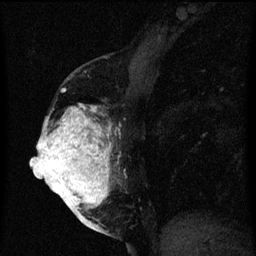
Breast MRI (dynamic contrast-enhanced), one sagittal slice. Position 26 of 60 along the scan axis. Dynamic contrast-enhanced series, image 2 of 3 at this slice position (ordered by acquisition). 1.5 T. TE 4.2 ms, TR 8 ms. 2 mm slice thickness. 256 × 256 image matrix, field of view 180 × 180 mm. Patient: female, 56 years.
Annotated regions visible in this slice (semi-automatic segmentation, software-assisted and operator-edited):
- analysis volume of interest (the breast-tissue region the enhancement analysis was run in; not a lesion): bounding box [x1, y1, x2, y2] px = [40, 106, 123, 219]
- tumour enhancement mask (voxels above the 70 % enhancement threshold inside the analysis volume of interest): [40, 106, 111, 219]